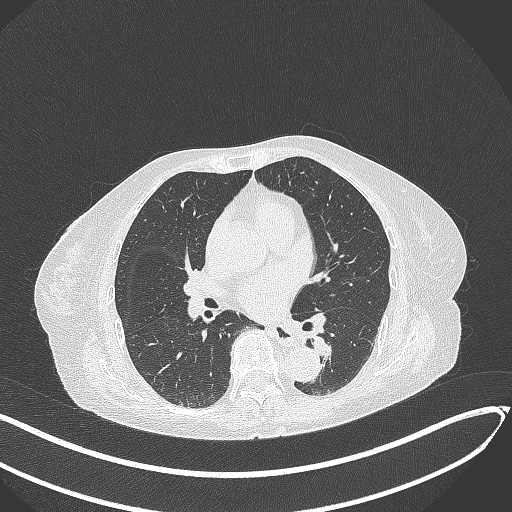
Chest CT, one axial slice. Position 128 of 324 along the scan axis. Reconstruction kernel B70f. Lung window (W 1500 / L -600 HU). 512 × 512 image matrix, field of view 400 × 400 mm. Female patient, age 82 years. From the clinical record (not read from this slice): clinical TNM (as recorded): T1b N0 M1.
Annotated regions visible in this slice (rectangle marked by the reading radiologist):
- lung tumour (recorded histology: adenocarcinoma): bounding box (x1, y1, x2, y2) in pixels: (310, 333, 344, 362)